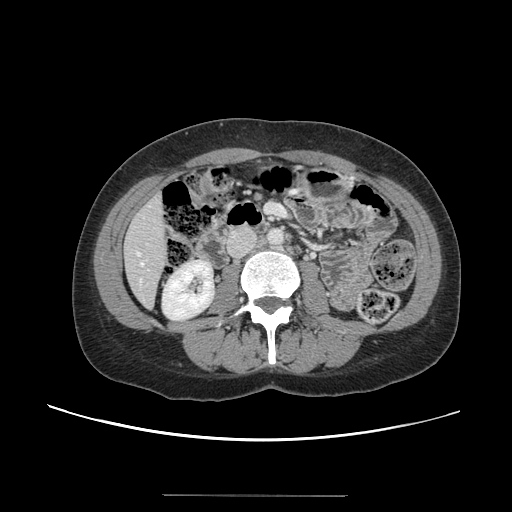
Contrast-enhanced abdominal CT, one axial slice. Position 37 of 144 along the scan axis. 120 kVp. Soft-tissue window (W 400 / L 40 HU). 512 × 512 image matrix. Female patient, age 53 years. From the clinical record (not read from this slice): diagnosis: colorectal cancer liver metastases, imaged before liver resection; multiple liver metastases: yes; largest metastasis: 1.1 cm; disease in both lobes: no.
Annotated regions visible in this slice (expert manual segmentation):
- hepatic veins: bounding box (x1, y1, x2, y2) in pixels: (137, 252, 144, 265)
- liver: (124, 195, 168, 307)
- planned liver remnant (the part of the liver to remain after resection): (125, 194, 168, 307)